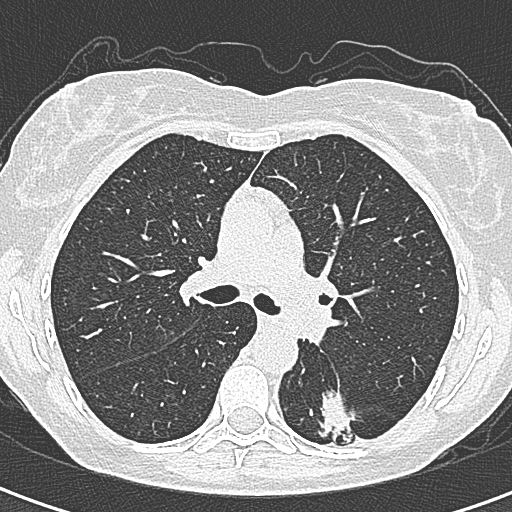
Chest CT (low-dose screening protocol), one axial image, baseline screening round, lung window (W 1500 / L -600 HU), 1 mm slice thickness, lung (sharp) reconstruction kernel (B80f), 120 kVp. Female participant, aged 58 years at enrolment. Former smoker at enrolment.
- Expert-annotated lung lesion, bounding box [x1, y1, x2, y2] px = [292, 390, 362, 455].
- The screening reader recorded 2 non-calcified nodules or masses ≥4 mm on this exam (left lower lobe, right lower lobe); which of them this box marks is not recorded.